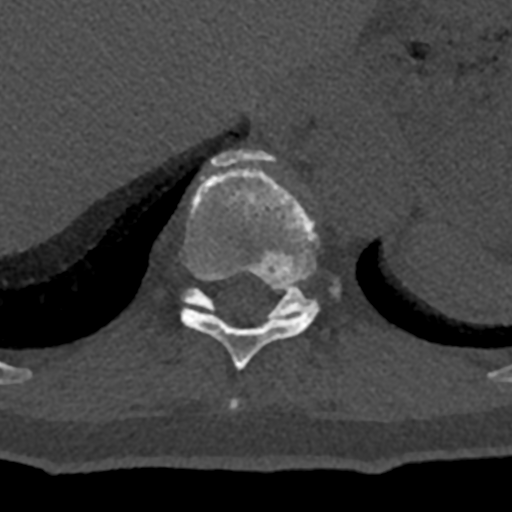
CT including the spine, one axial slice. Position 589 of 797 along the scan axis. Reconstruction kernel Br40s/3. 120 kVp. Bone window (W 1800 / L 400 HU). 0.5 mm slice thickness. 512 × 512 image matrix, field of view 160 × 160 mm. Male patient, age 74 years. From the clinical record (not read from this slice): primary cancer: renal.
Outlined on this slice (semi-automatic segmentation, software-assisted and operator-edited):
- T10 vertebra: bounding box [x1, y1, x2, y2] px = [180, 149, 320, 370]
- T11 vertebra: [182, 279, 340, 319]
- T9 vertebra: [231, 399, 239, 408]